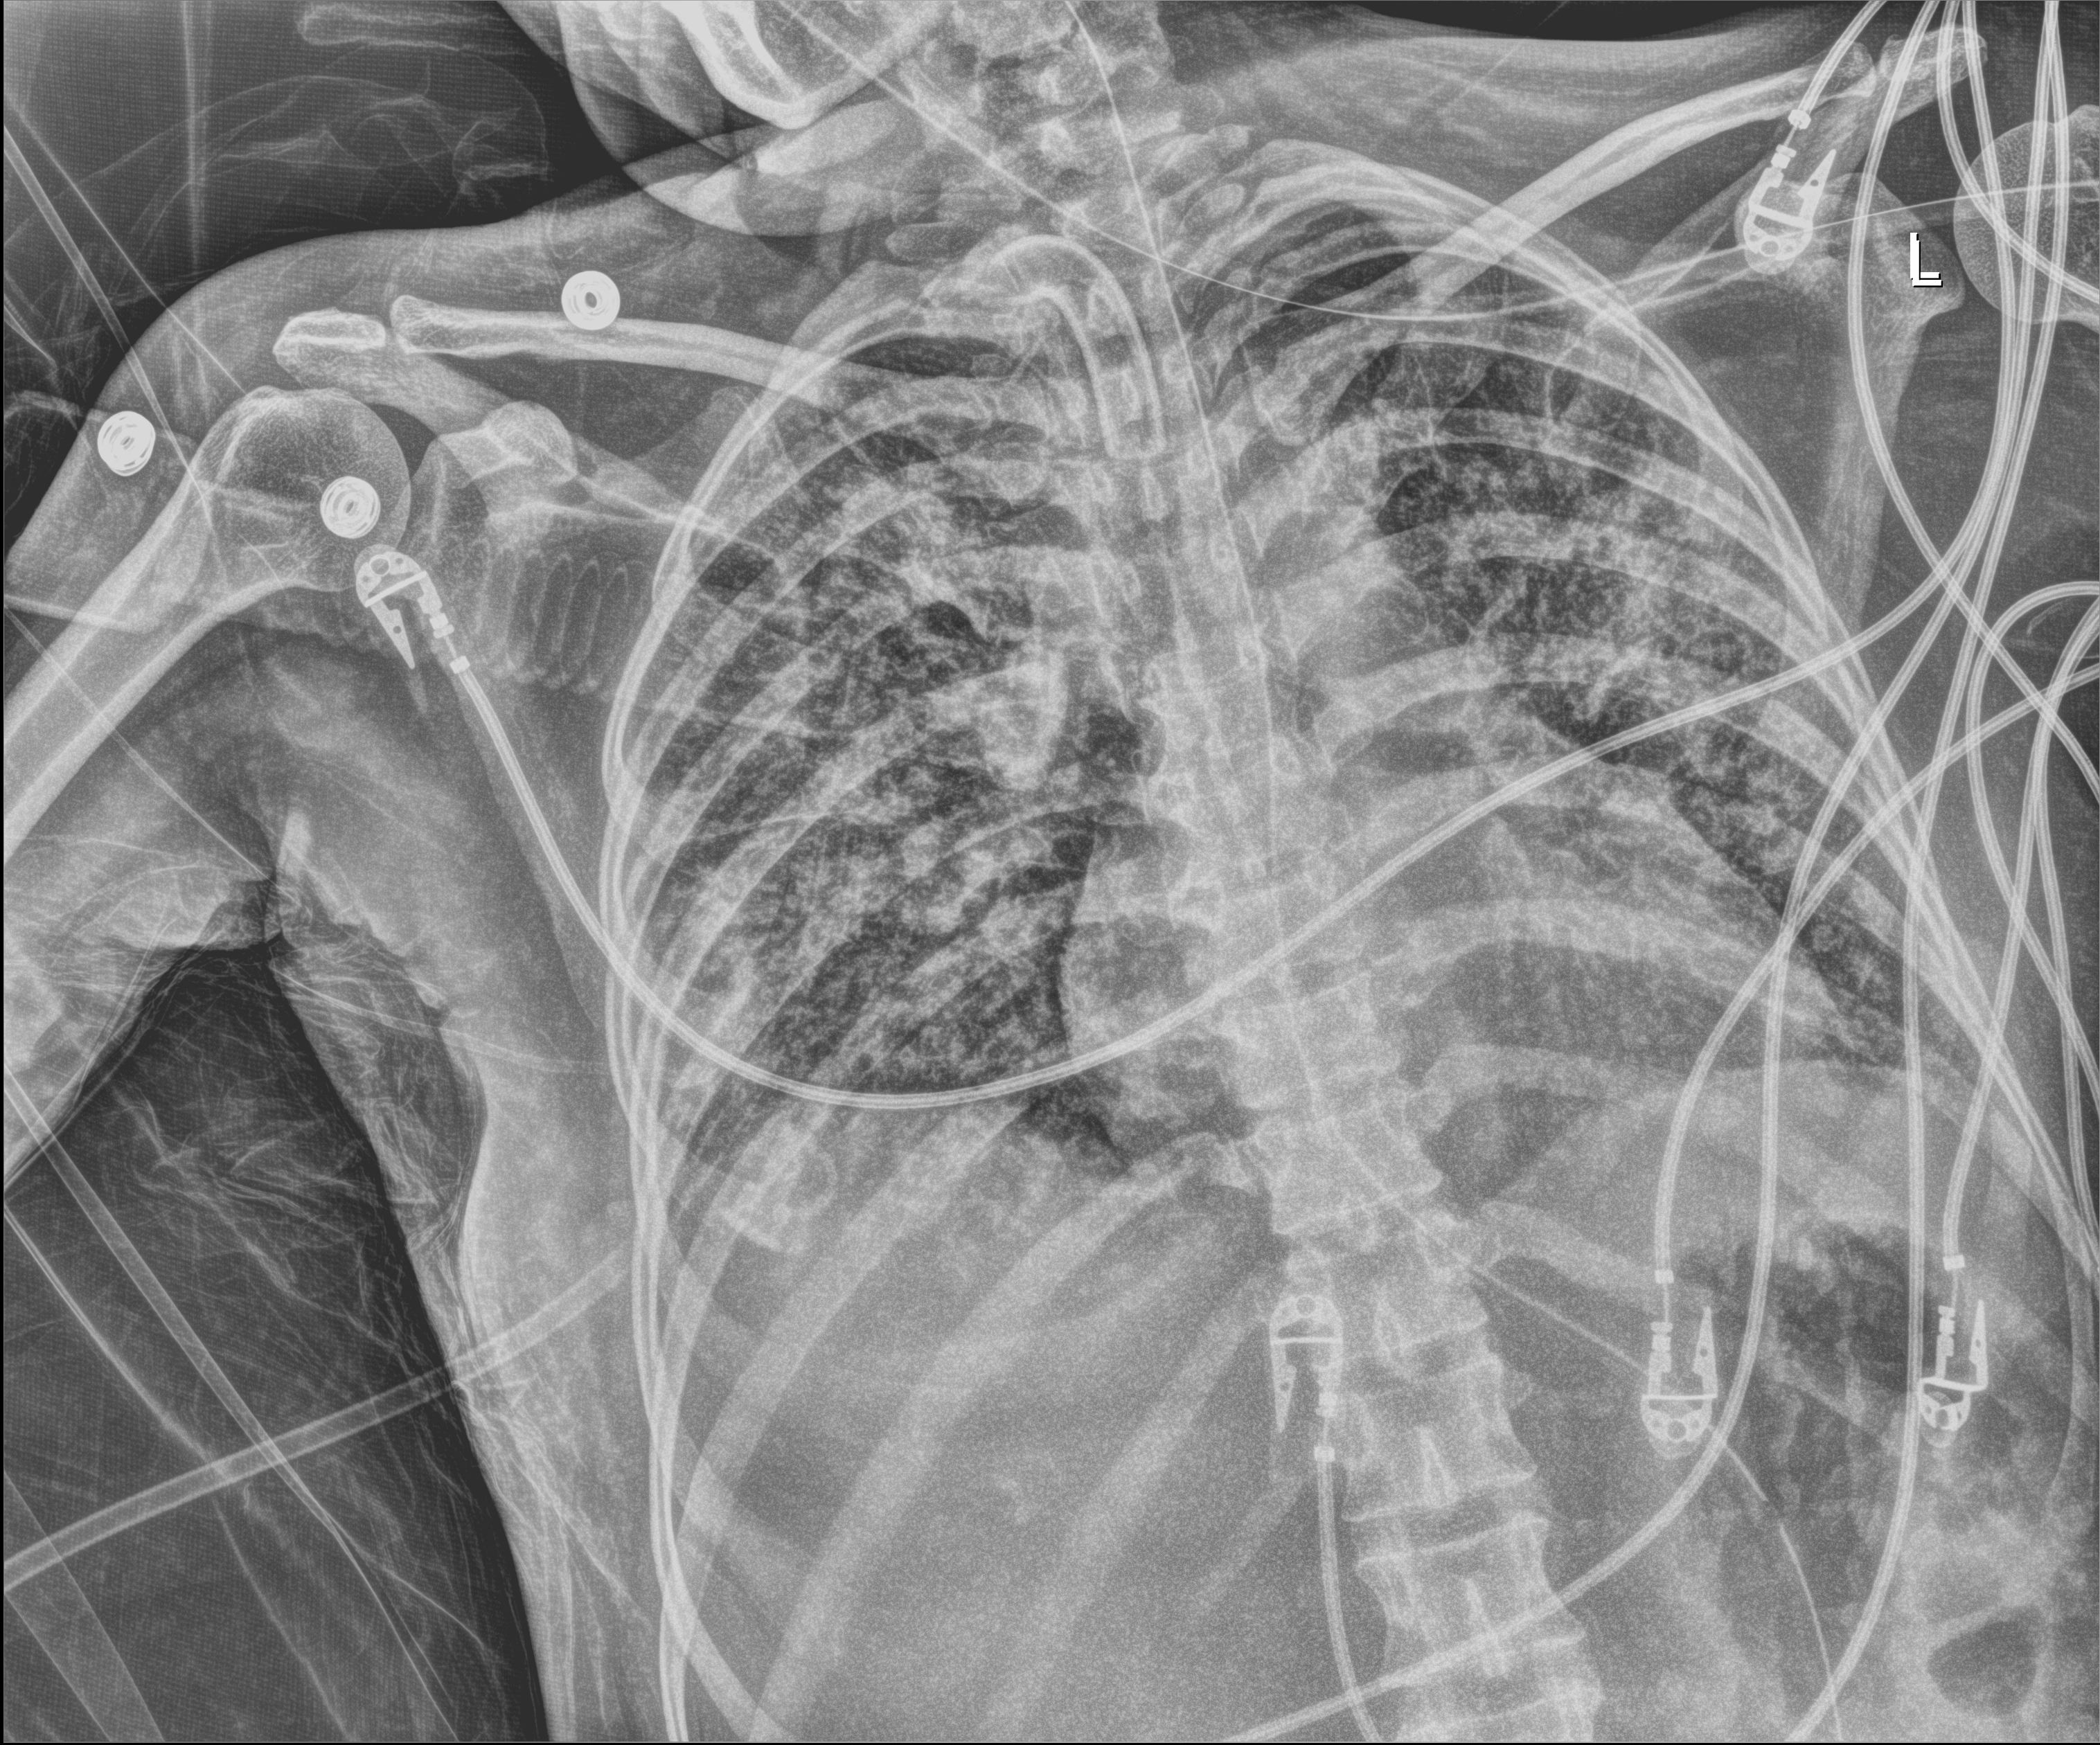
Bedside chest radiograph (digital radiography), anteroposterior (AP) projection. Female patient hospitalised with COVID-19, age 18–59 years.
From the hospital-stay record, not from the radiograph (when in the stay this image was taken is not recorded): hypertension (admission record): no; other chronic lung disease (admission record): no; mechanically ventilated during this hospital stay: yes.